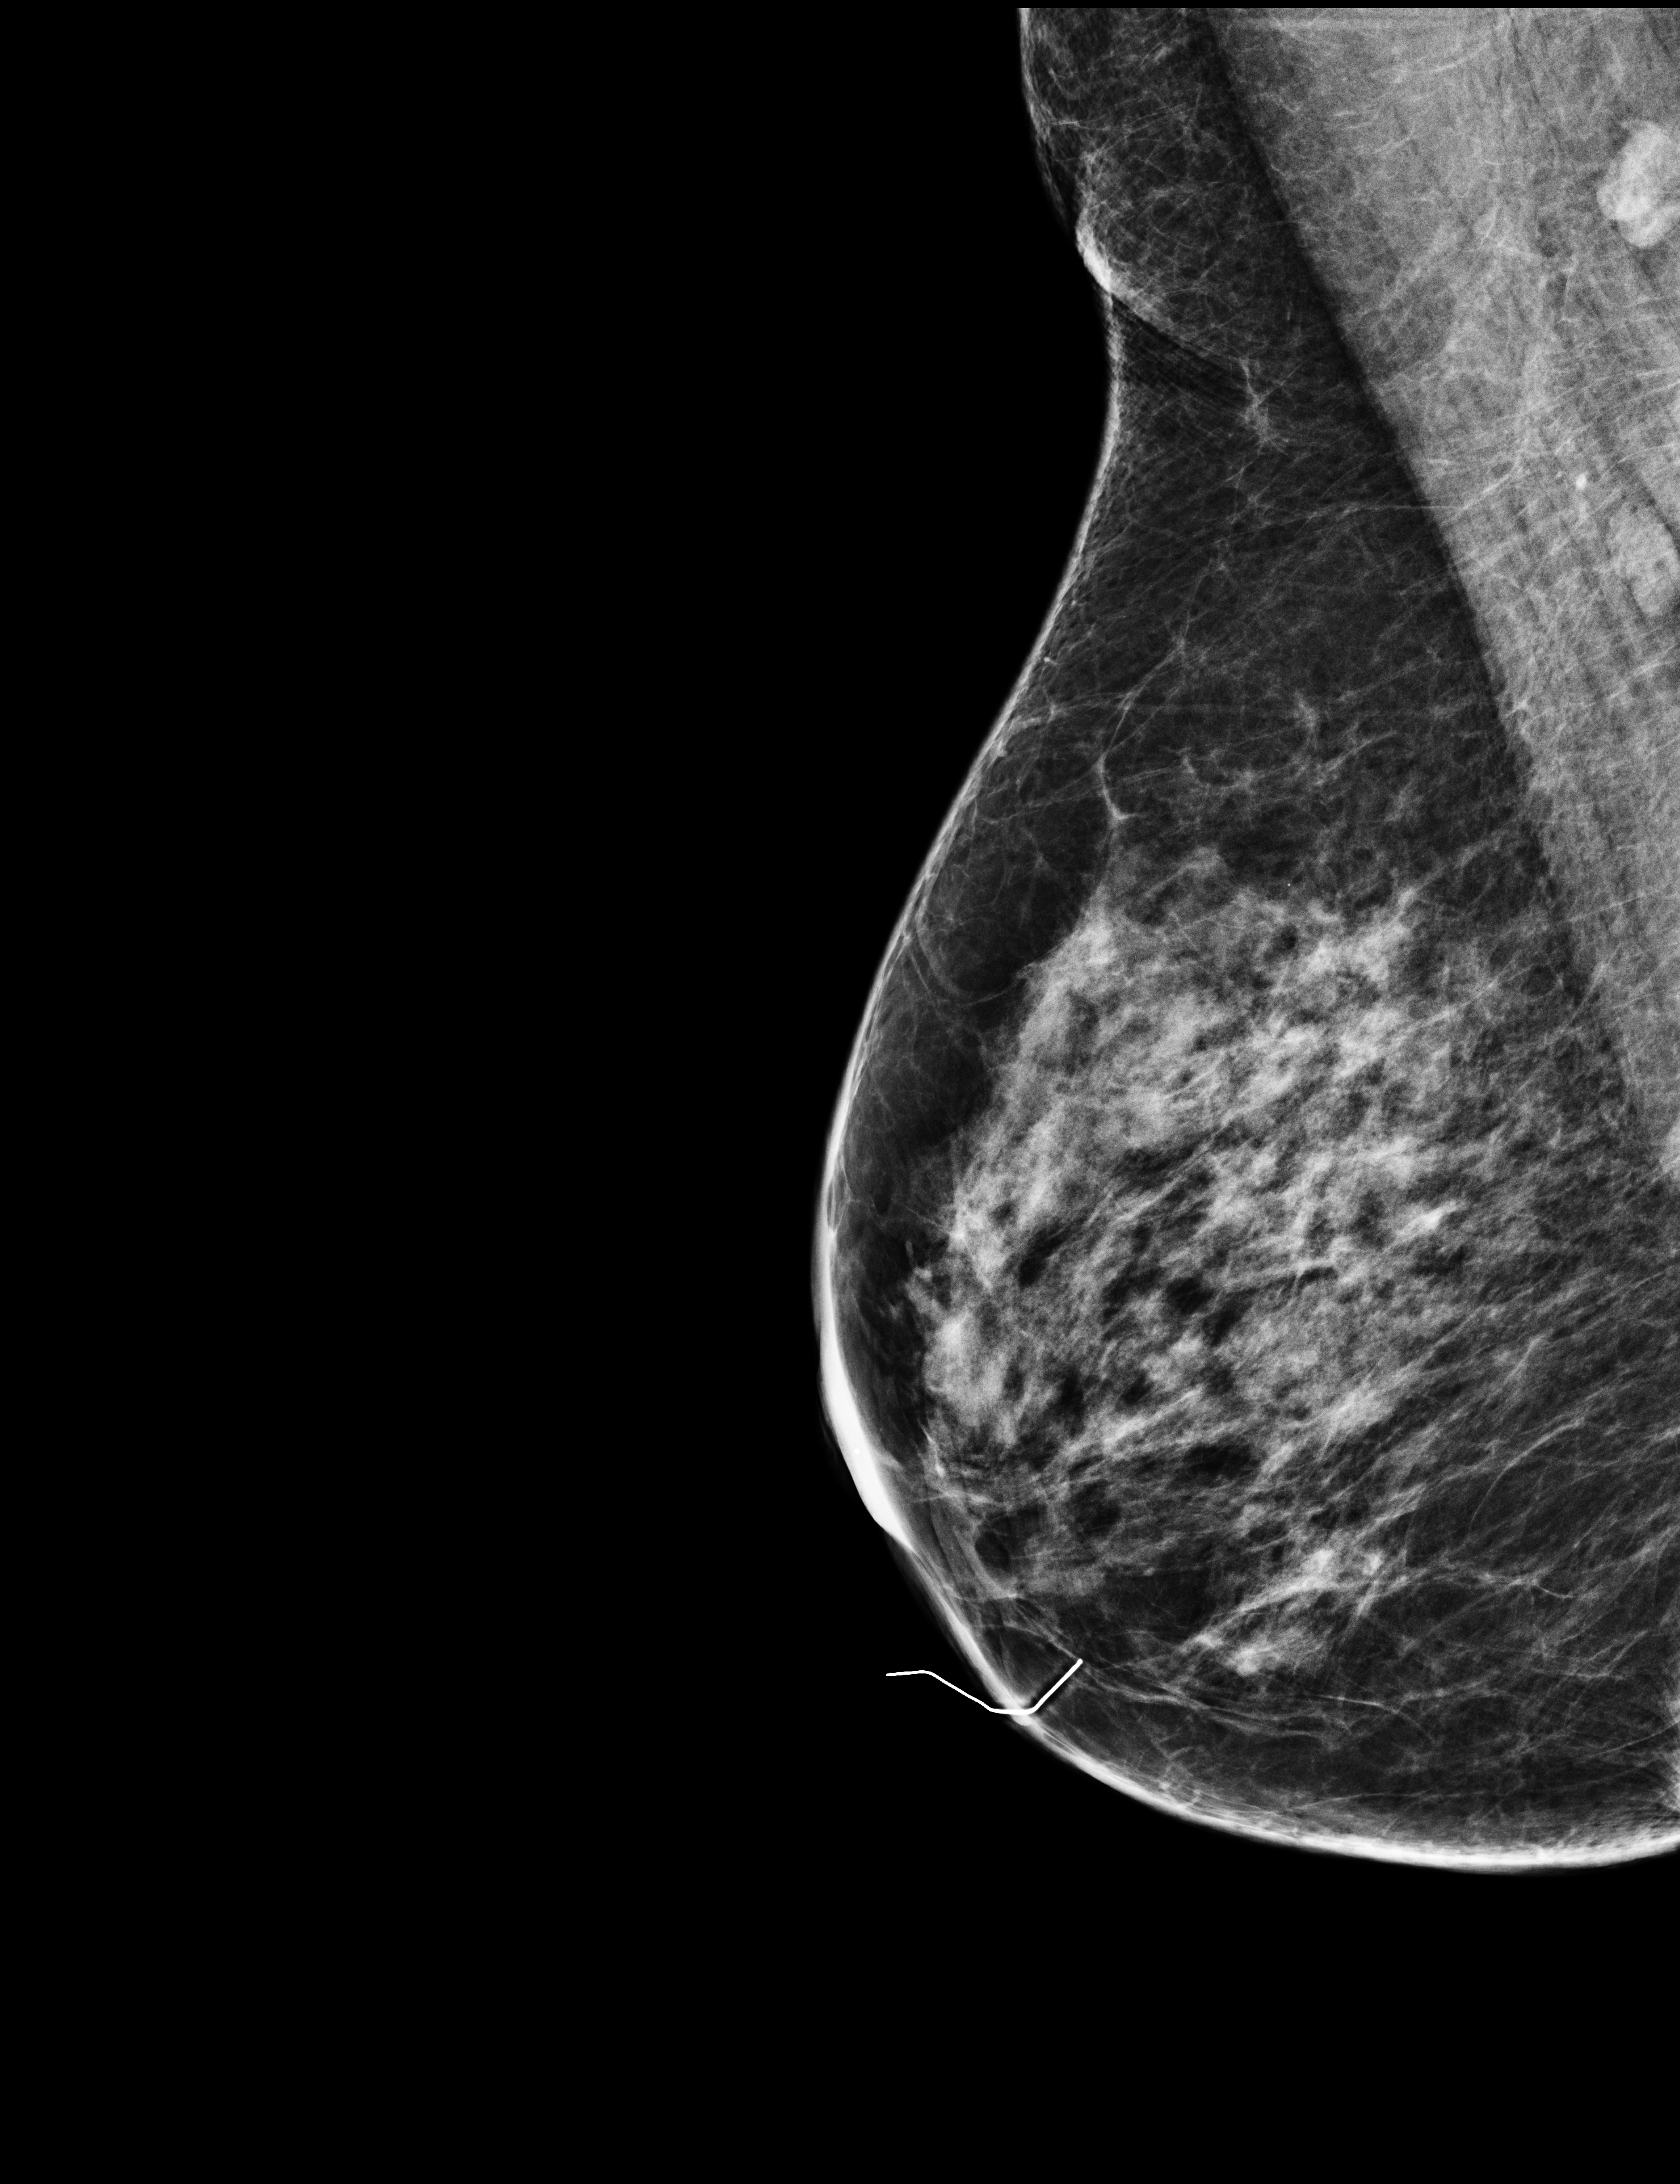
Digital mammogram (FFDM), right breast, mediolateral oblique (MLO) view, screening examination, system: Selenia Dimensions. Patient aged 60 years (female).
Final BI-RADS assessment for this screening round (tomosynthesis exam, both breasts): category 1.